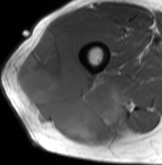
MRI of an extremity soft-tissue mass, one axial slice; position 52 of 61 along the scan axis; MR volume resampled by the dataset authors to the PET/CT grid (not the native acquisition matrix); 3.27 mm slice thickness; 162 × 165 image matrix, field of view 158 × 161 mm. Male patient. From the clinical record (not read from this slice): histological type: poorly differentiated synovial sarcoma; grade: high; site of the primary tumour: right buttock.
Annotated regions visible in this slice (expert contour drawn on MRI and transferred to this co-registered scan by the dataset authors):
- gross tumour volume including surrounding oedema: bounding box <14,29,122,144> (left, top, right, bottom; pixels)
- gross tumour volume (mass): <14,29,122,144>